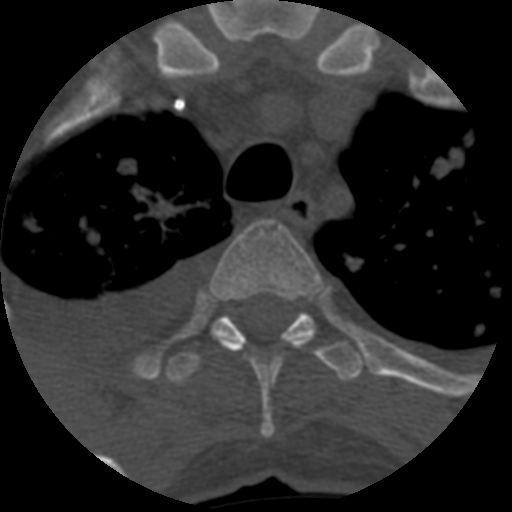
CT including the spine, one axial slice. Position 481 of 708 along the scan axis. One of 3 acquisitions stored at this slice position. Bone window (W 1800 / L 400 HU). 1.25 mm slice thickness. 512 × 512 image matrix, field of view 160 × 160 mm. Patient age 55 years. Case-level facts recorded for this patient, not image findings: primary cancer: colon; vertebrae with lytic lesions (as recorded): T12, L1, L5.
Outlined on this slice (semi-automatic segmentation, software-assisted and operator-edited):
- T3 vertebra: bounding box (x1, y1, x2, y2) in pixels: (212, 220, 321, 438)
- T4 vertebra: (165, 312, 364, 385)